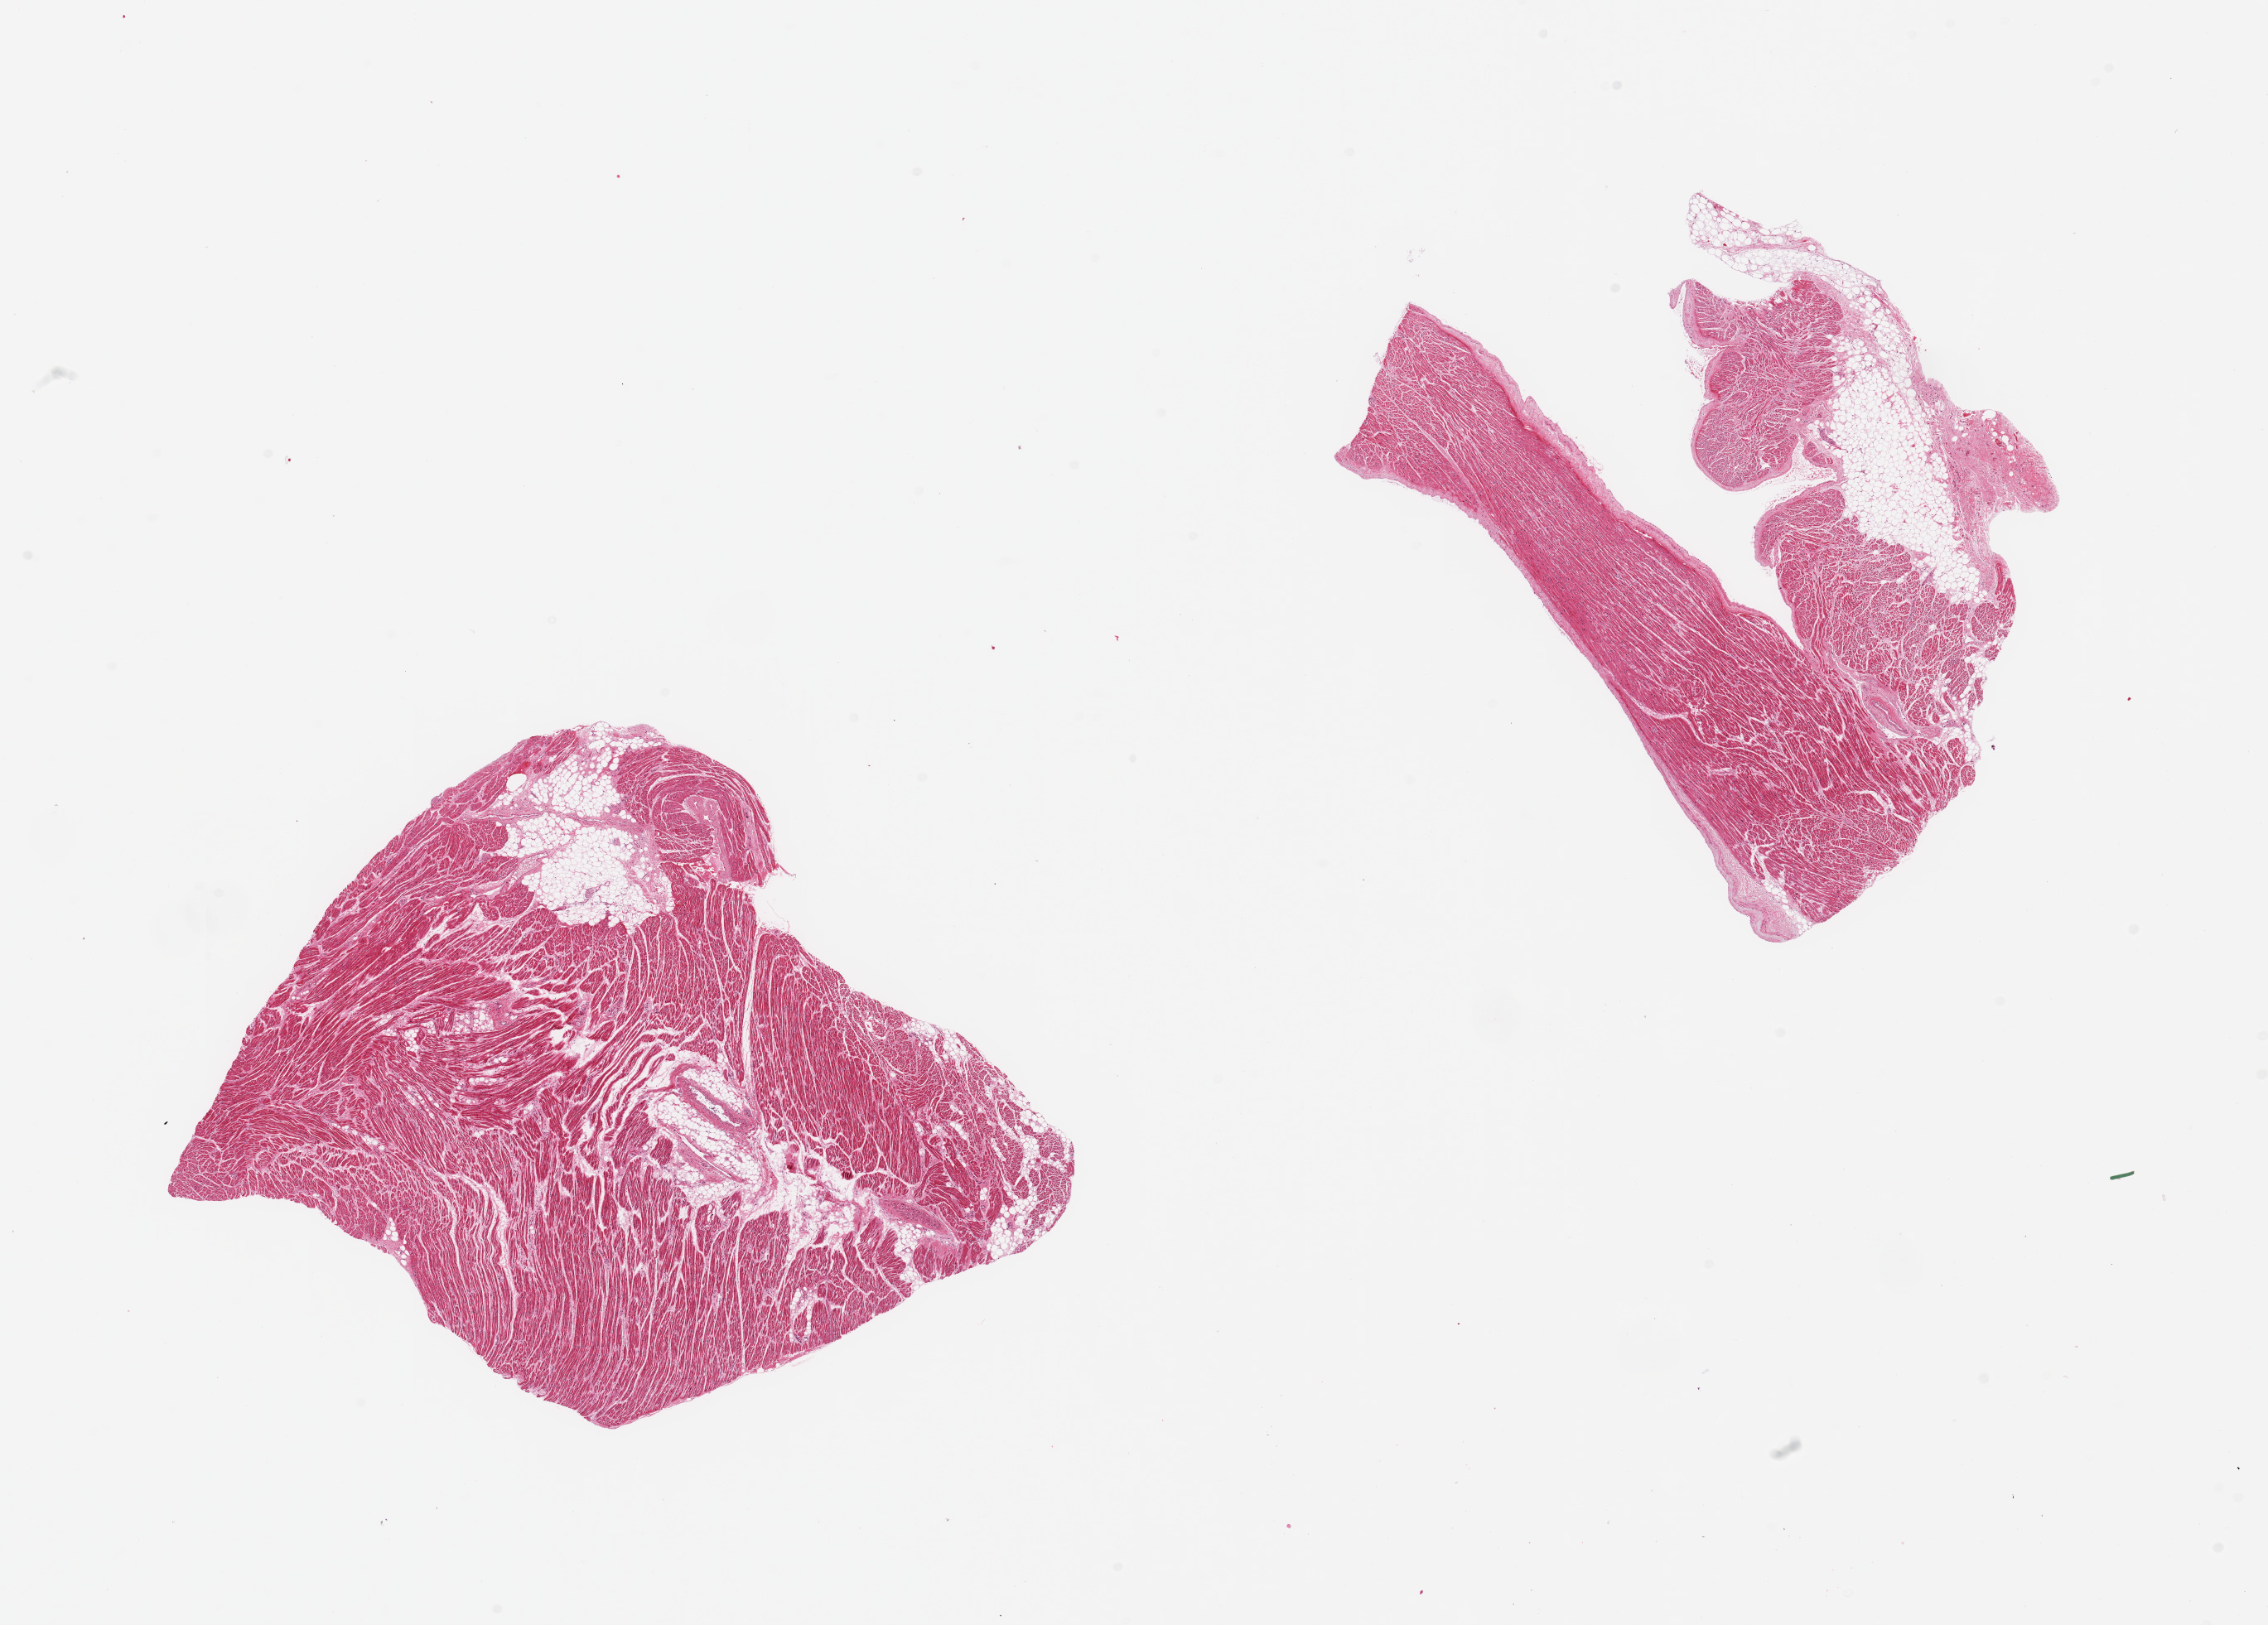
Digitized haematoxylin and eosin-stained section, whole scanned area (about 21.7 x 15.5 mm) shown as a low-resolution overview; PAXgene-fixed paraffin-embedded (PFPE) section; target tissue: auricular appendage; donor tissue sample. Male donor.
Reviewer comment on this tissue sample: 2 pieces; 10 & 20% fat content.